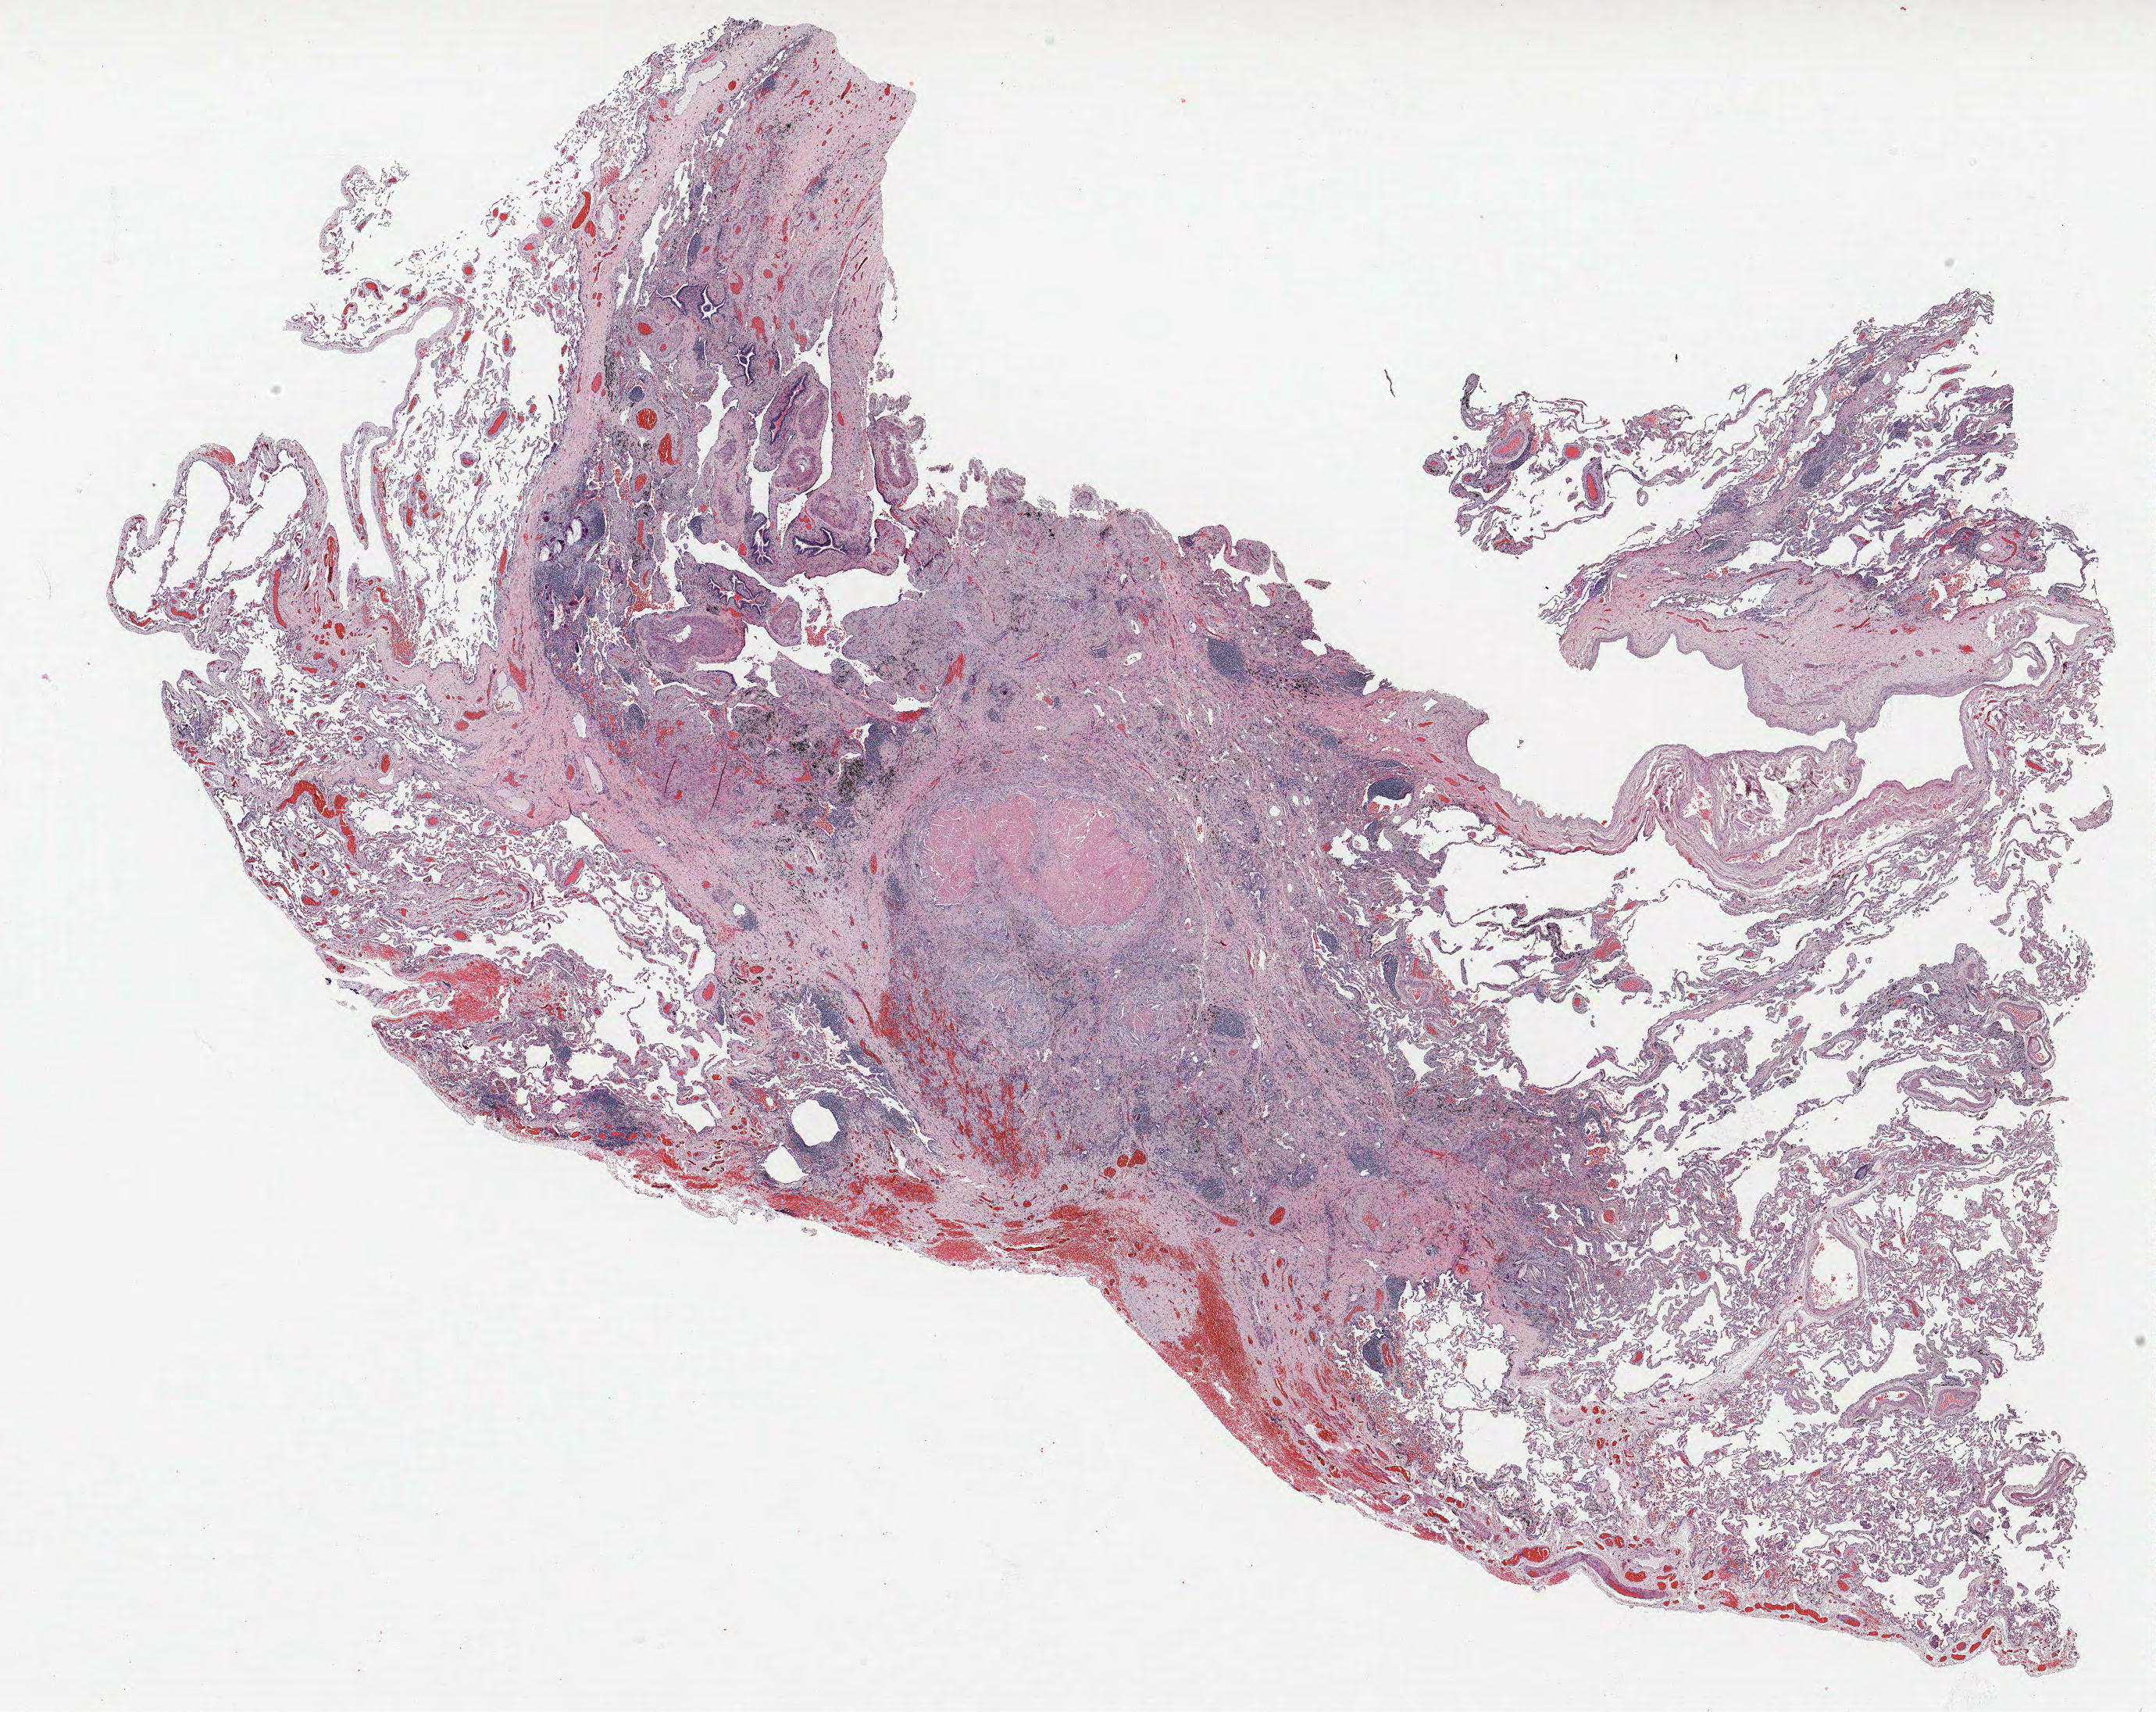
Hematoxylin and eosin (H&E) stained whole-slide image, a low-resolution overview of the entire scanned area, about 22.1 x 17.5 mm (from a 40x scan); FFPE section; lung. Female, age 59 at enrolment. Current smoker at enrolment. Grade: moderately differentiated (G2).
- stage (AJCC 6th edition): IA
- participant's lung-cancer diagnosis: Squamous cell carcinoma, NOS
- primary tumour location (clinical record): right upper lobe
- tumour size (pathology): 28 mm